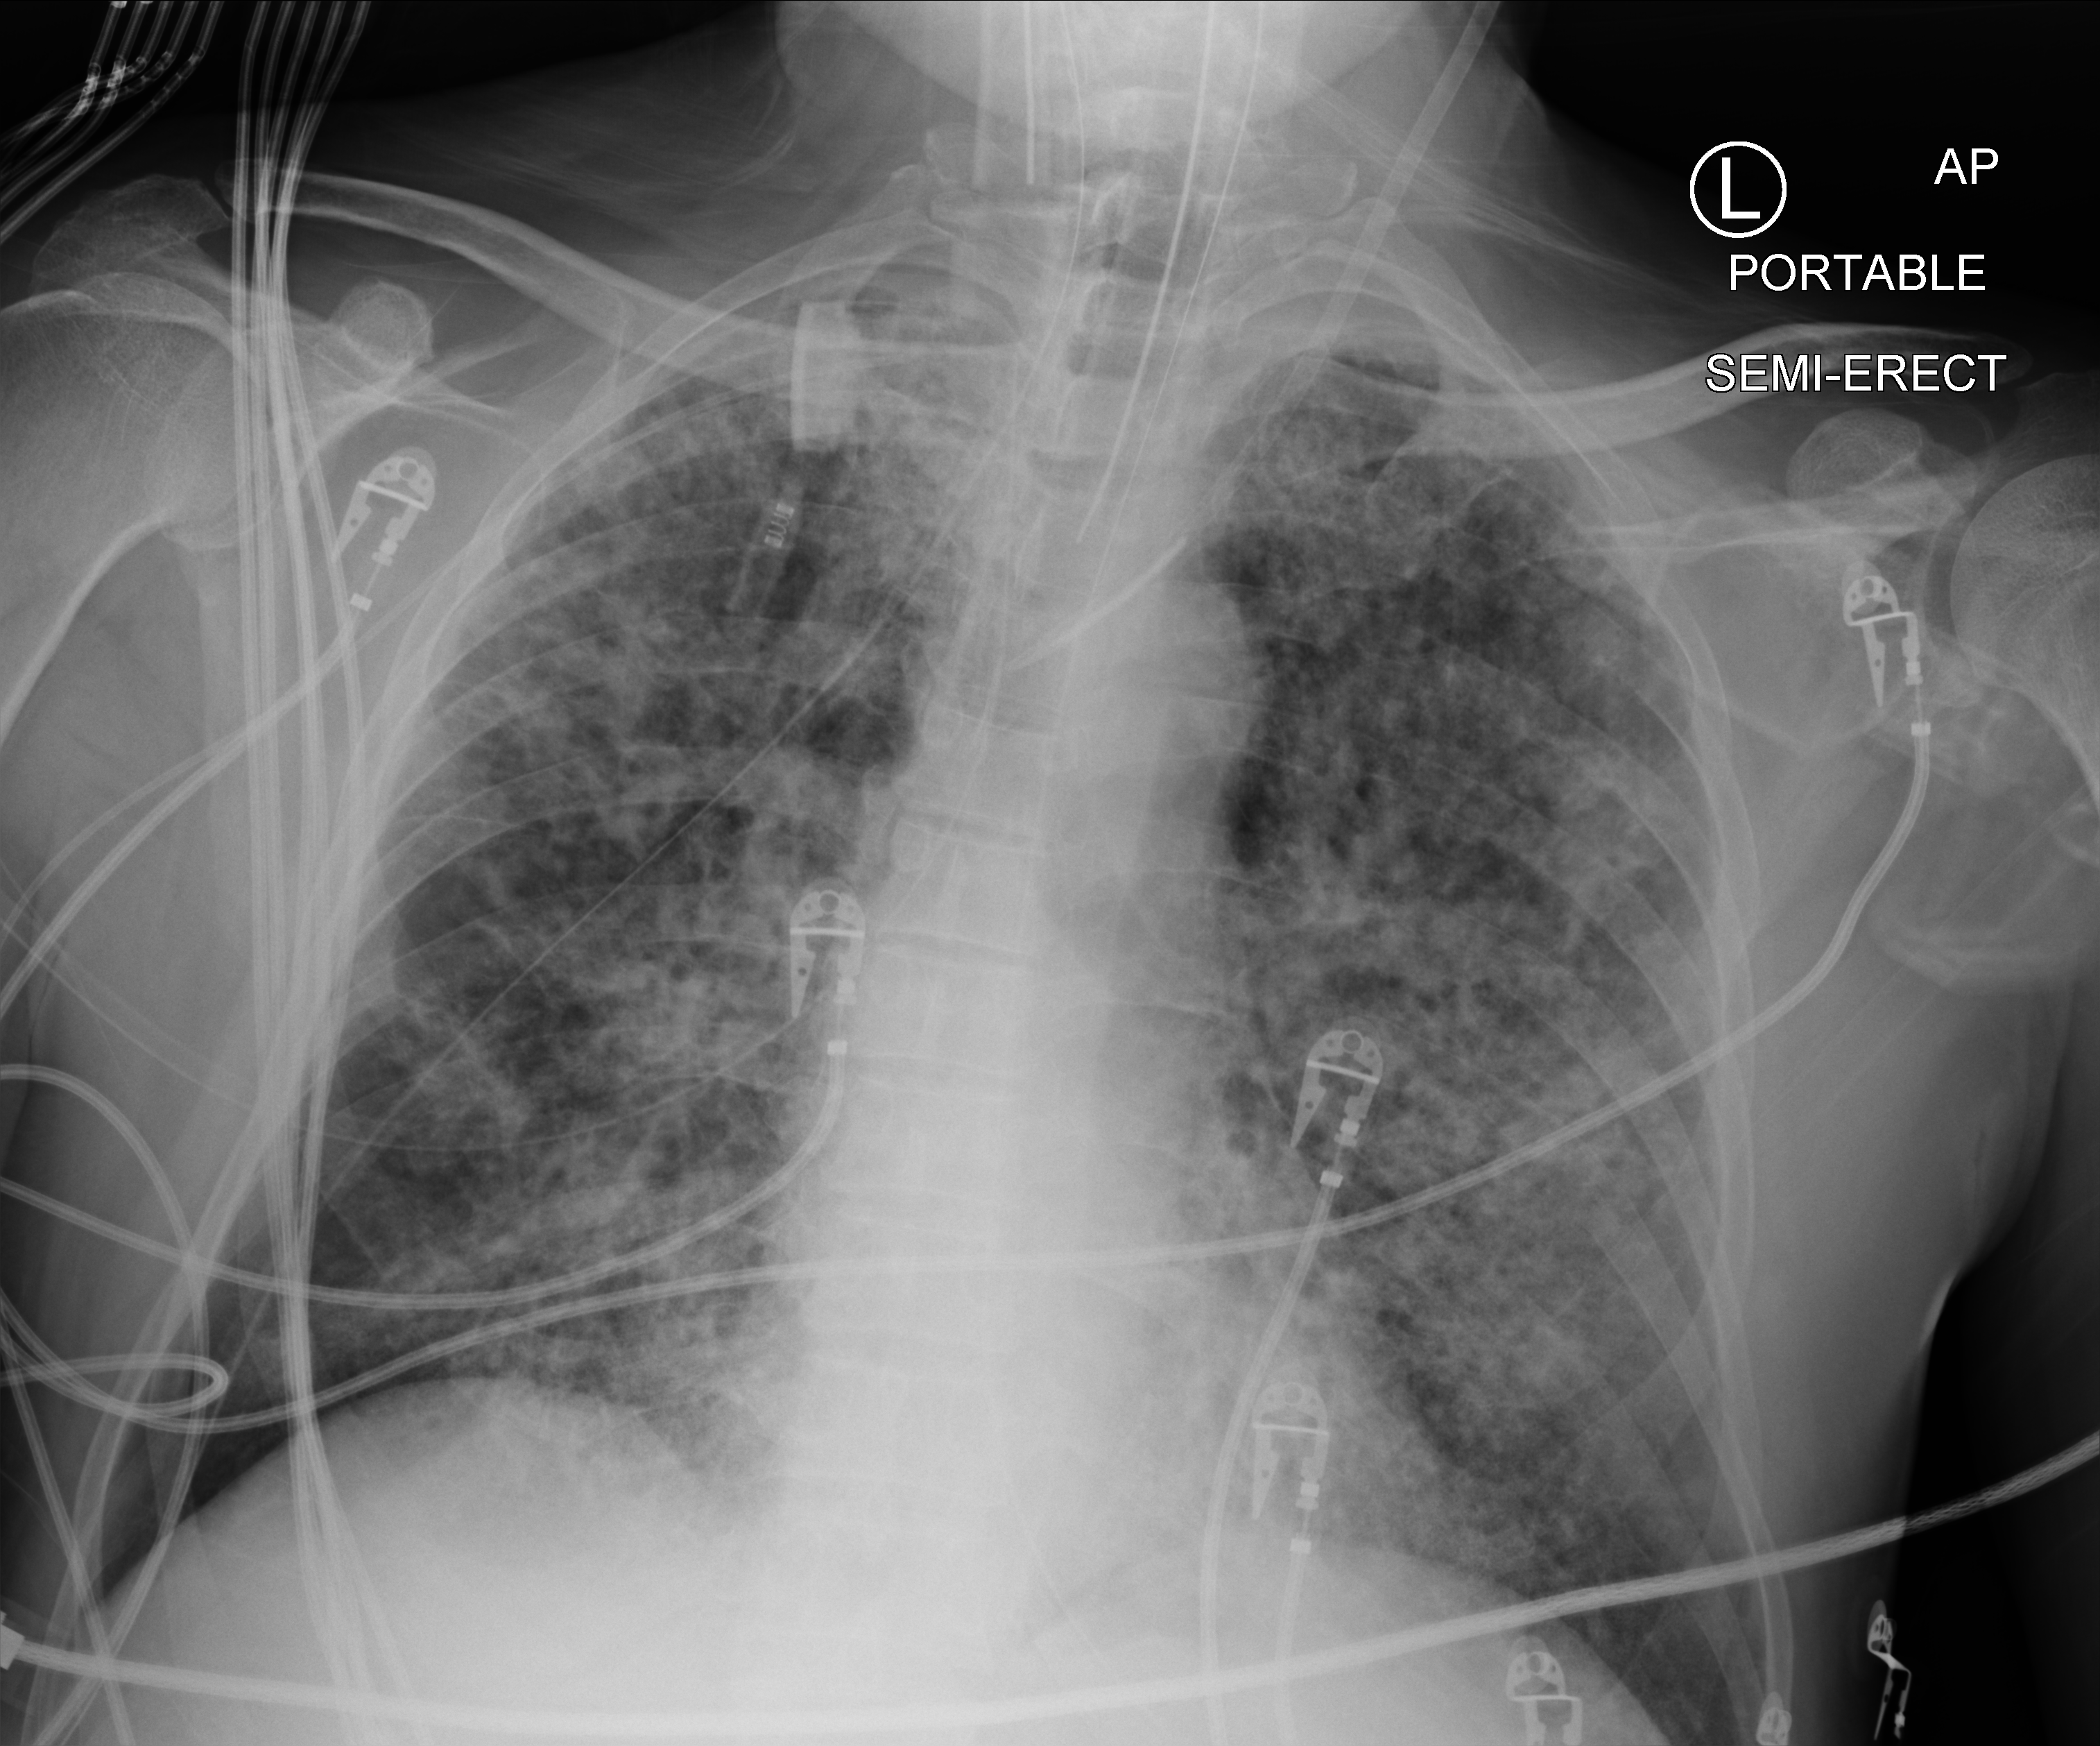
Chest X-ray (portable); anteroposterior (AP) projection. Patient hospitalised with COVID-19; male, aged 60–74 years.
From the hospital-stay record, not from the radiograph (when in the stay this image was taken is not recorded):
- length of hospital stay: 6 days
- admitted to intensive care during this hospital stay: yes